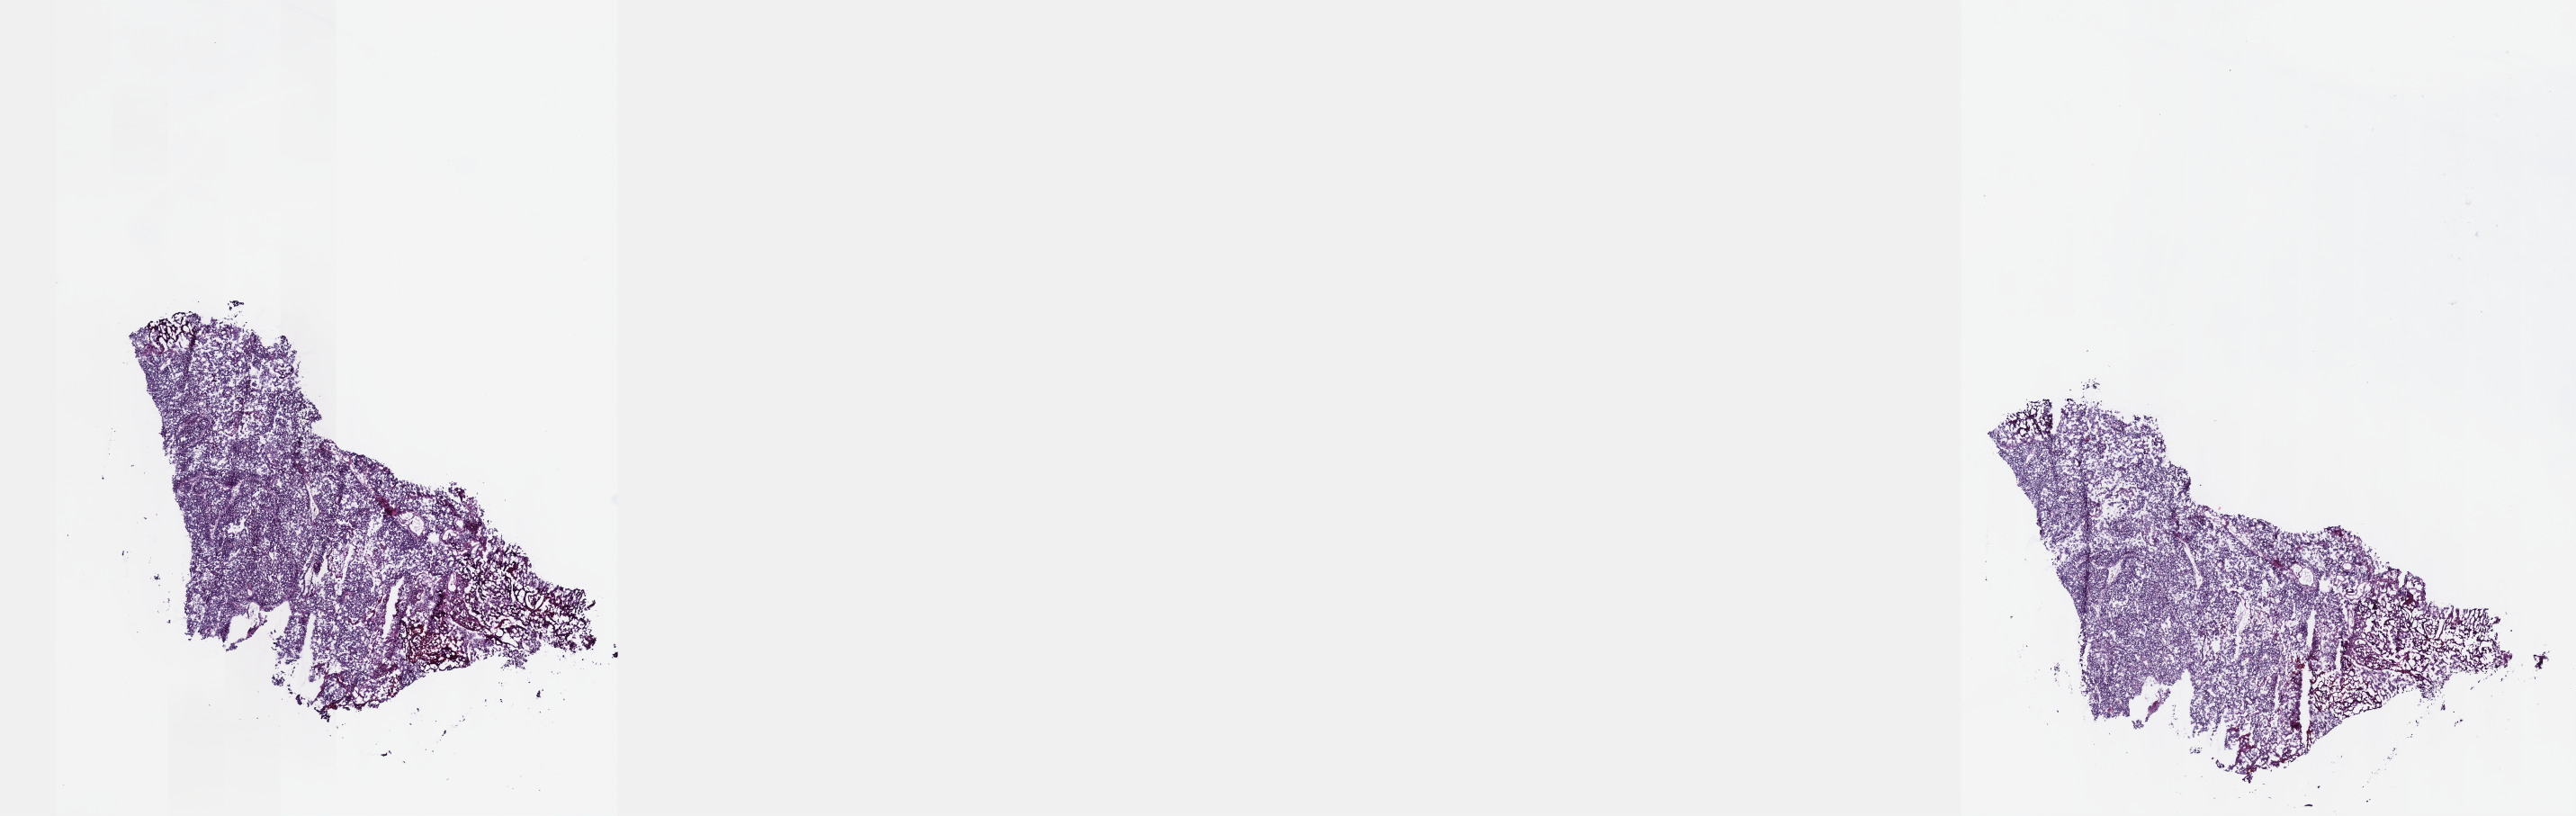
Digitized Hematoxylin and eosin (H&E) stained tissue section (whole slide), low-resolution overview of the scanned area, about 23.1 x 7.3 mm. Frozen section. Sample: primary tumour, bladder. Patient: male, age at initial diagnosis 83 years. Histologic grade: high grade. Composition of this section per pathologist review: tumour cells 100%, tumour nuclei 80%, normal cells 0%, stromal cells 0%, necrosis 0%. Inflammatory infiltration, as recorded: lymphocyte infiltration 2%, monocyte infiltration 0%, neutrophil infiltration 0%.
AJCC pathologic stage: II (7th edition). Pathologic diagnosis: Transitional cell carcinoma. TNM: T2 NX M0.